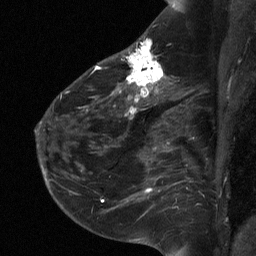
Breast MRI (dynamic contrast-enhanced), one sagittal slice; slice 42 of 64 in the series (ordered by position); dynamic contrast-enhanced study with each time point stored as its own series, time point 2 of 3 at this slice position (early post-contrast, ordered by acquisition time); 1.5 T; TE 4.8 ms, TR 27 ms; 256 × 256 image matrix, field of view 180 × 180 mm. Patient: female, 51 years. From the clinical record (not read from this slice): setting: breast cancer imaged before/during neoadjuvant chemotherapy; receptor status: HR-positive, HER2-negative.
Structures marked on this image (semi-automatic segmentation, software-assisted and operator-edited):
- analysis volume of interest (the breast-tissue region the enhancement analysis was run in; not a lesion): bounding box <72,34,182,118> (left, top, right, bottom; pixels)
- tumour enhancement mask (voxels above the 90 % enhancement threshold inside the analysis volume of interest): <95,38,164,118>